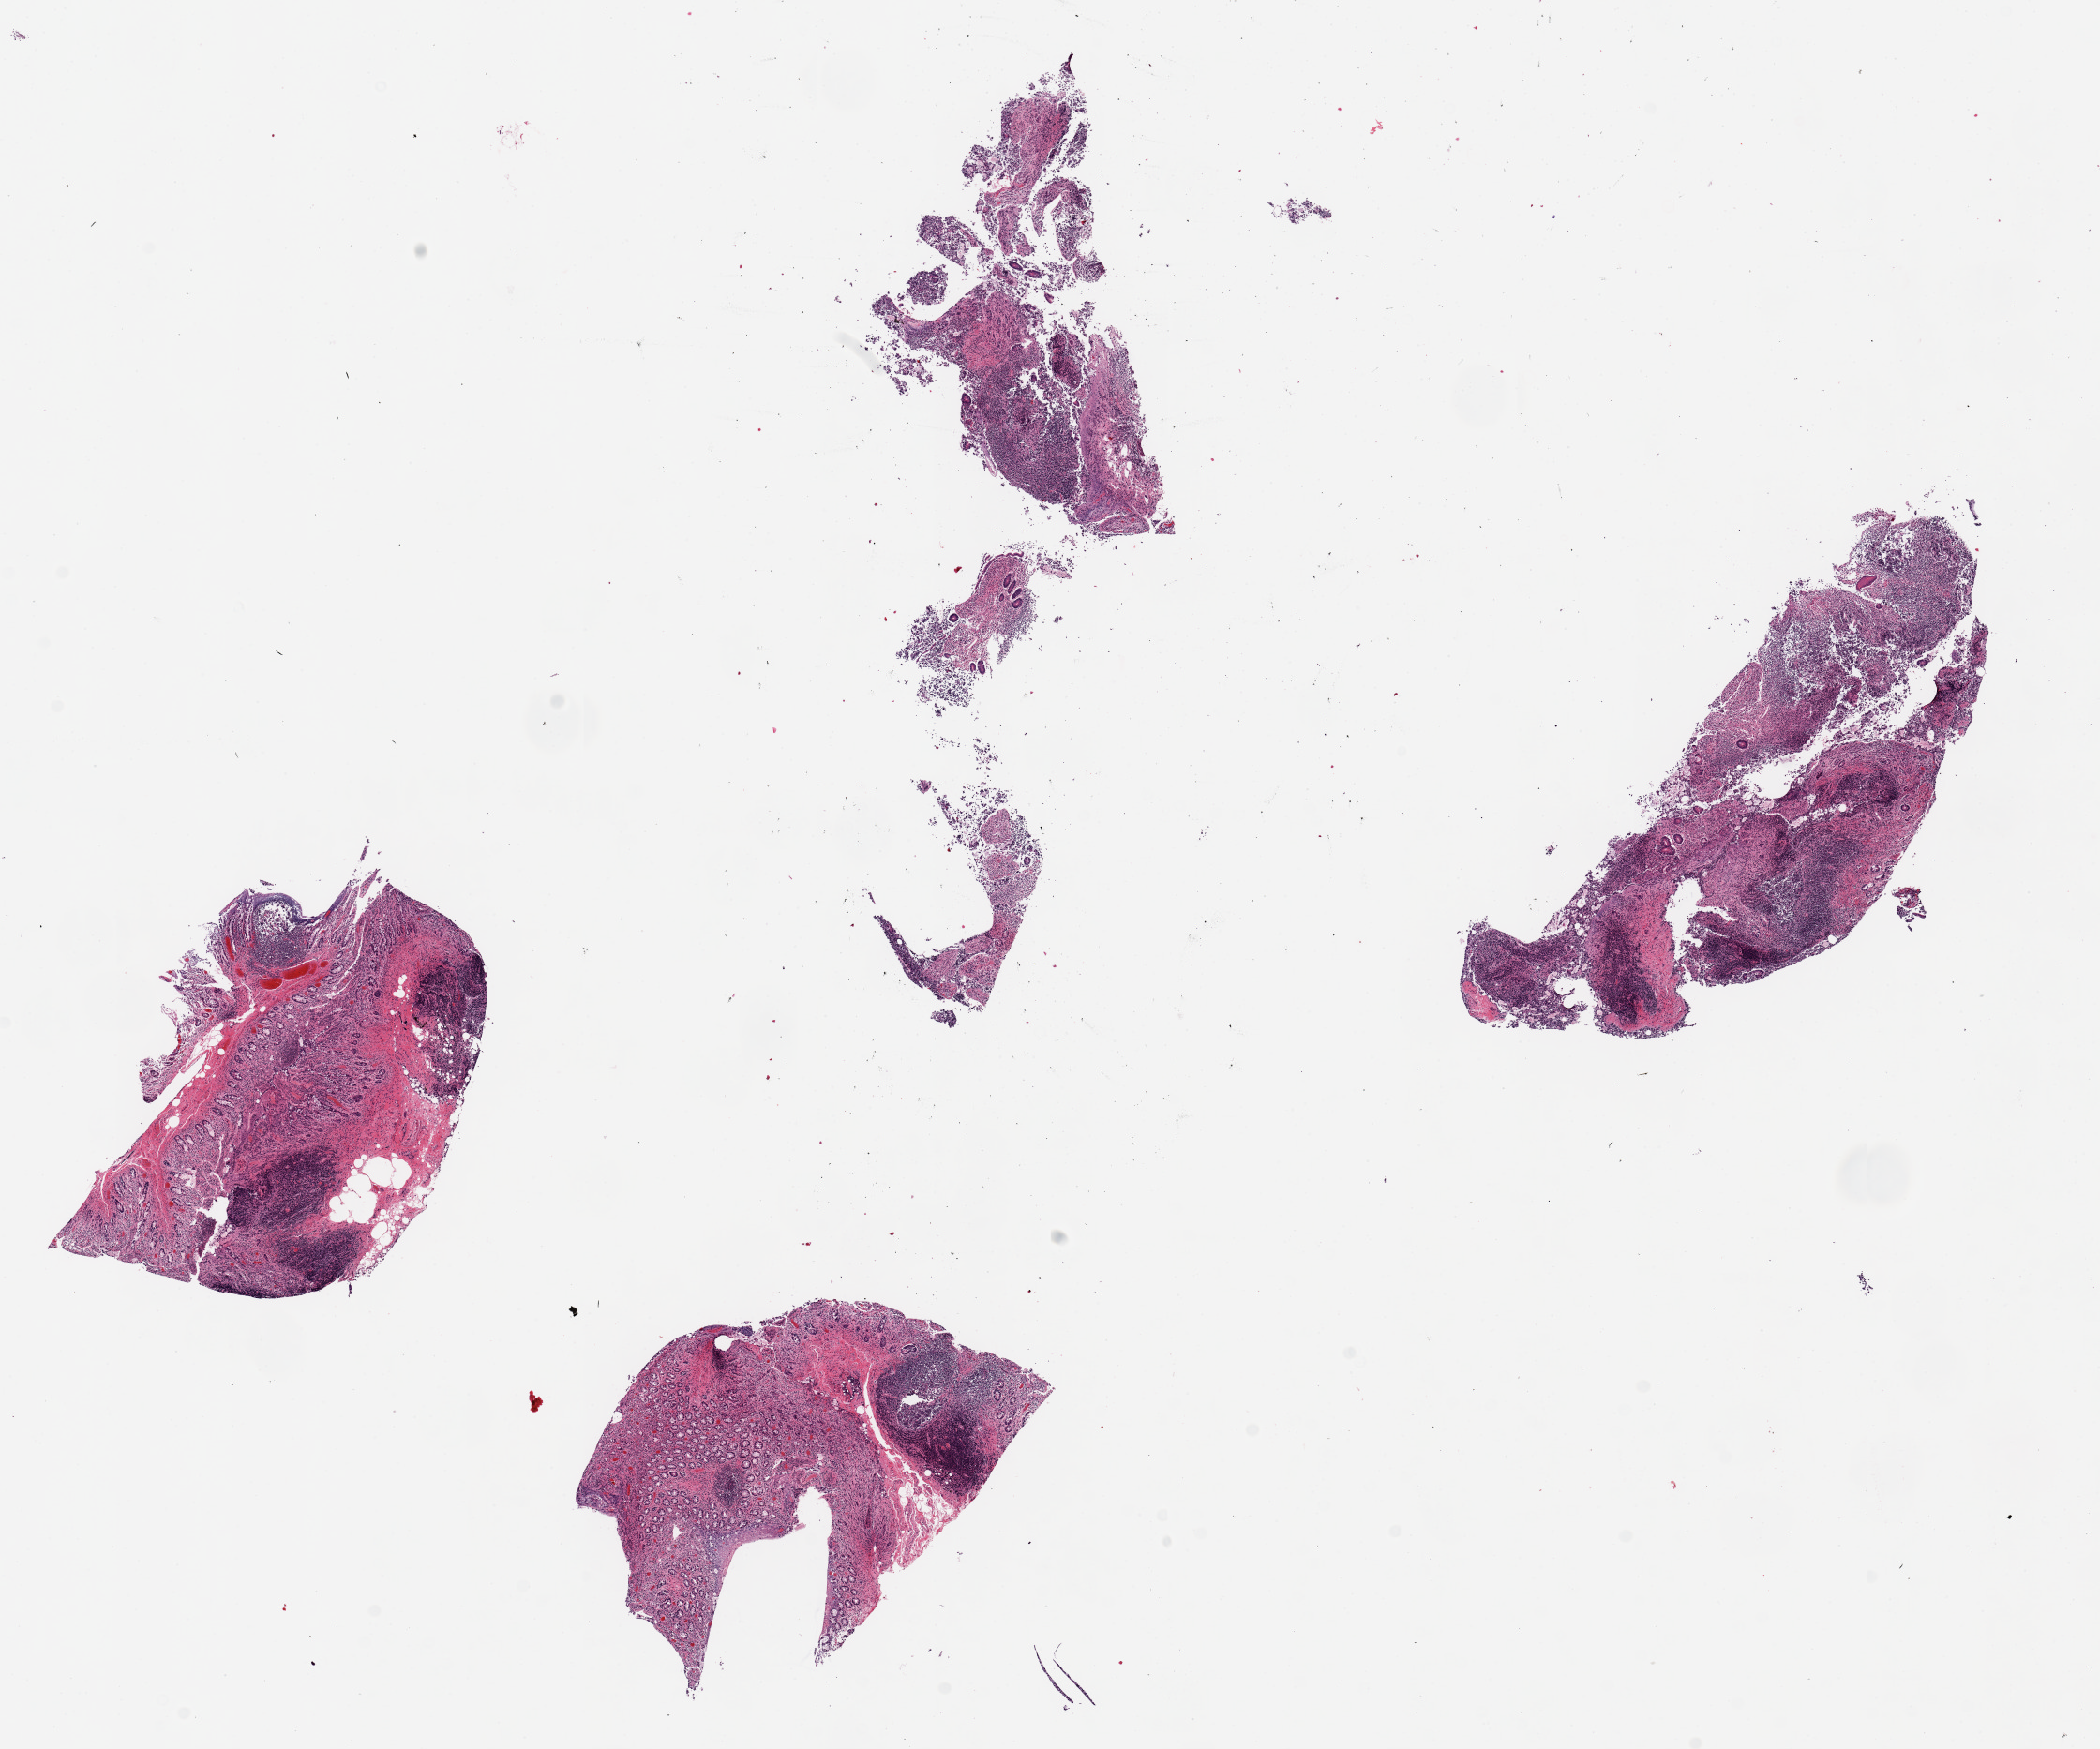
Haematoxylin and eosin whole-slide image — whole scanned area (about 17.7 x 14.8 mm) shown as a low-resolution overview. PAXgene-fixed paraffin-embedded (PFPE) section. Target tissue: ileum. Donor tissue sample. Male donor.
Pathologist's review note for this sample: 4 pieces, up to 8x3mm; moderate-severe autolysis, ~30% lymphoid elements, good specimen.